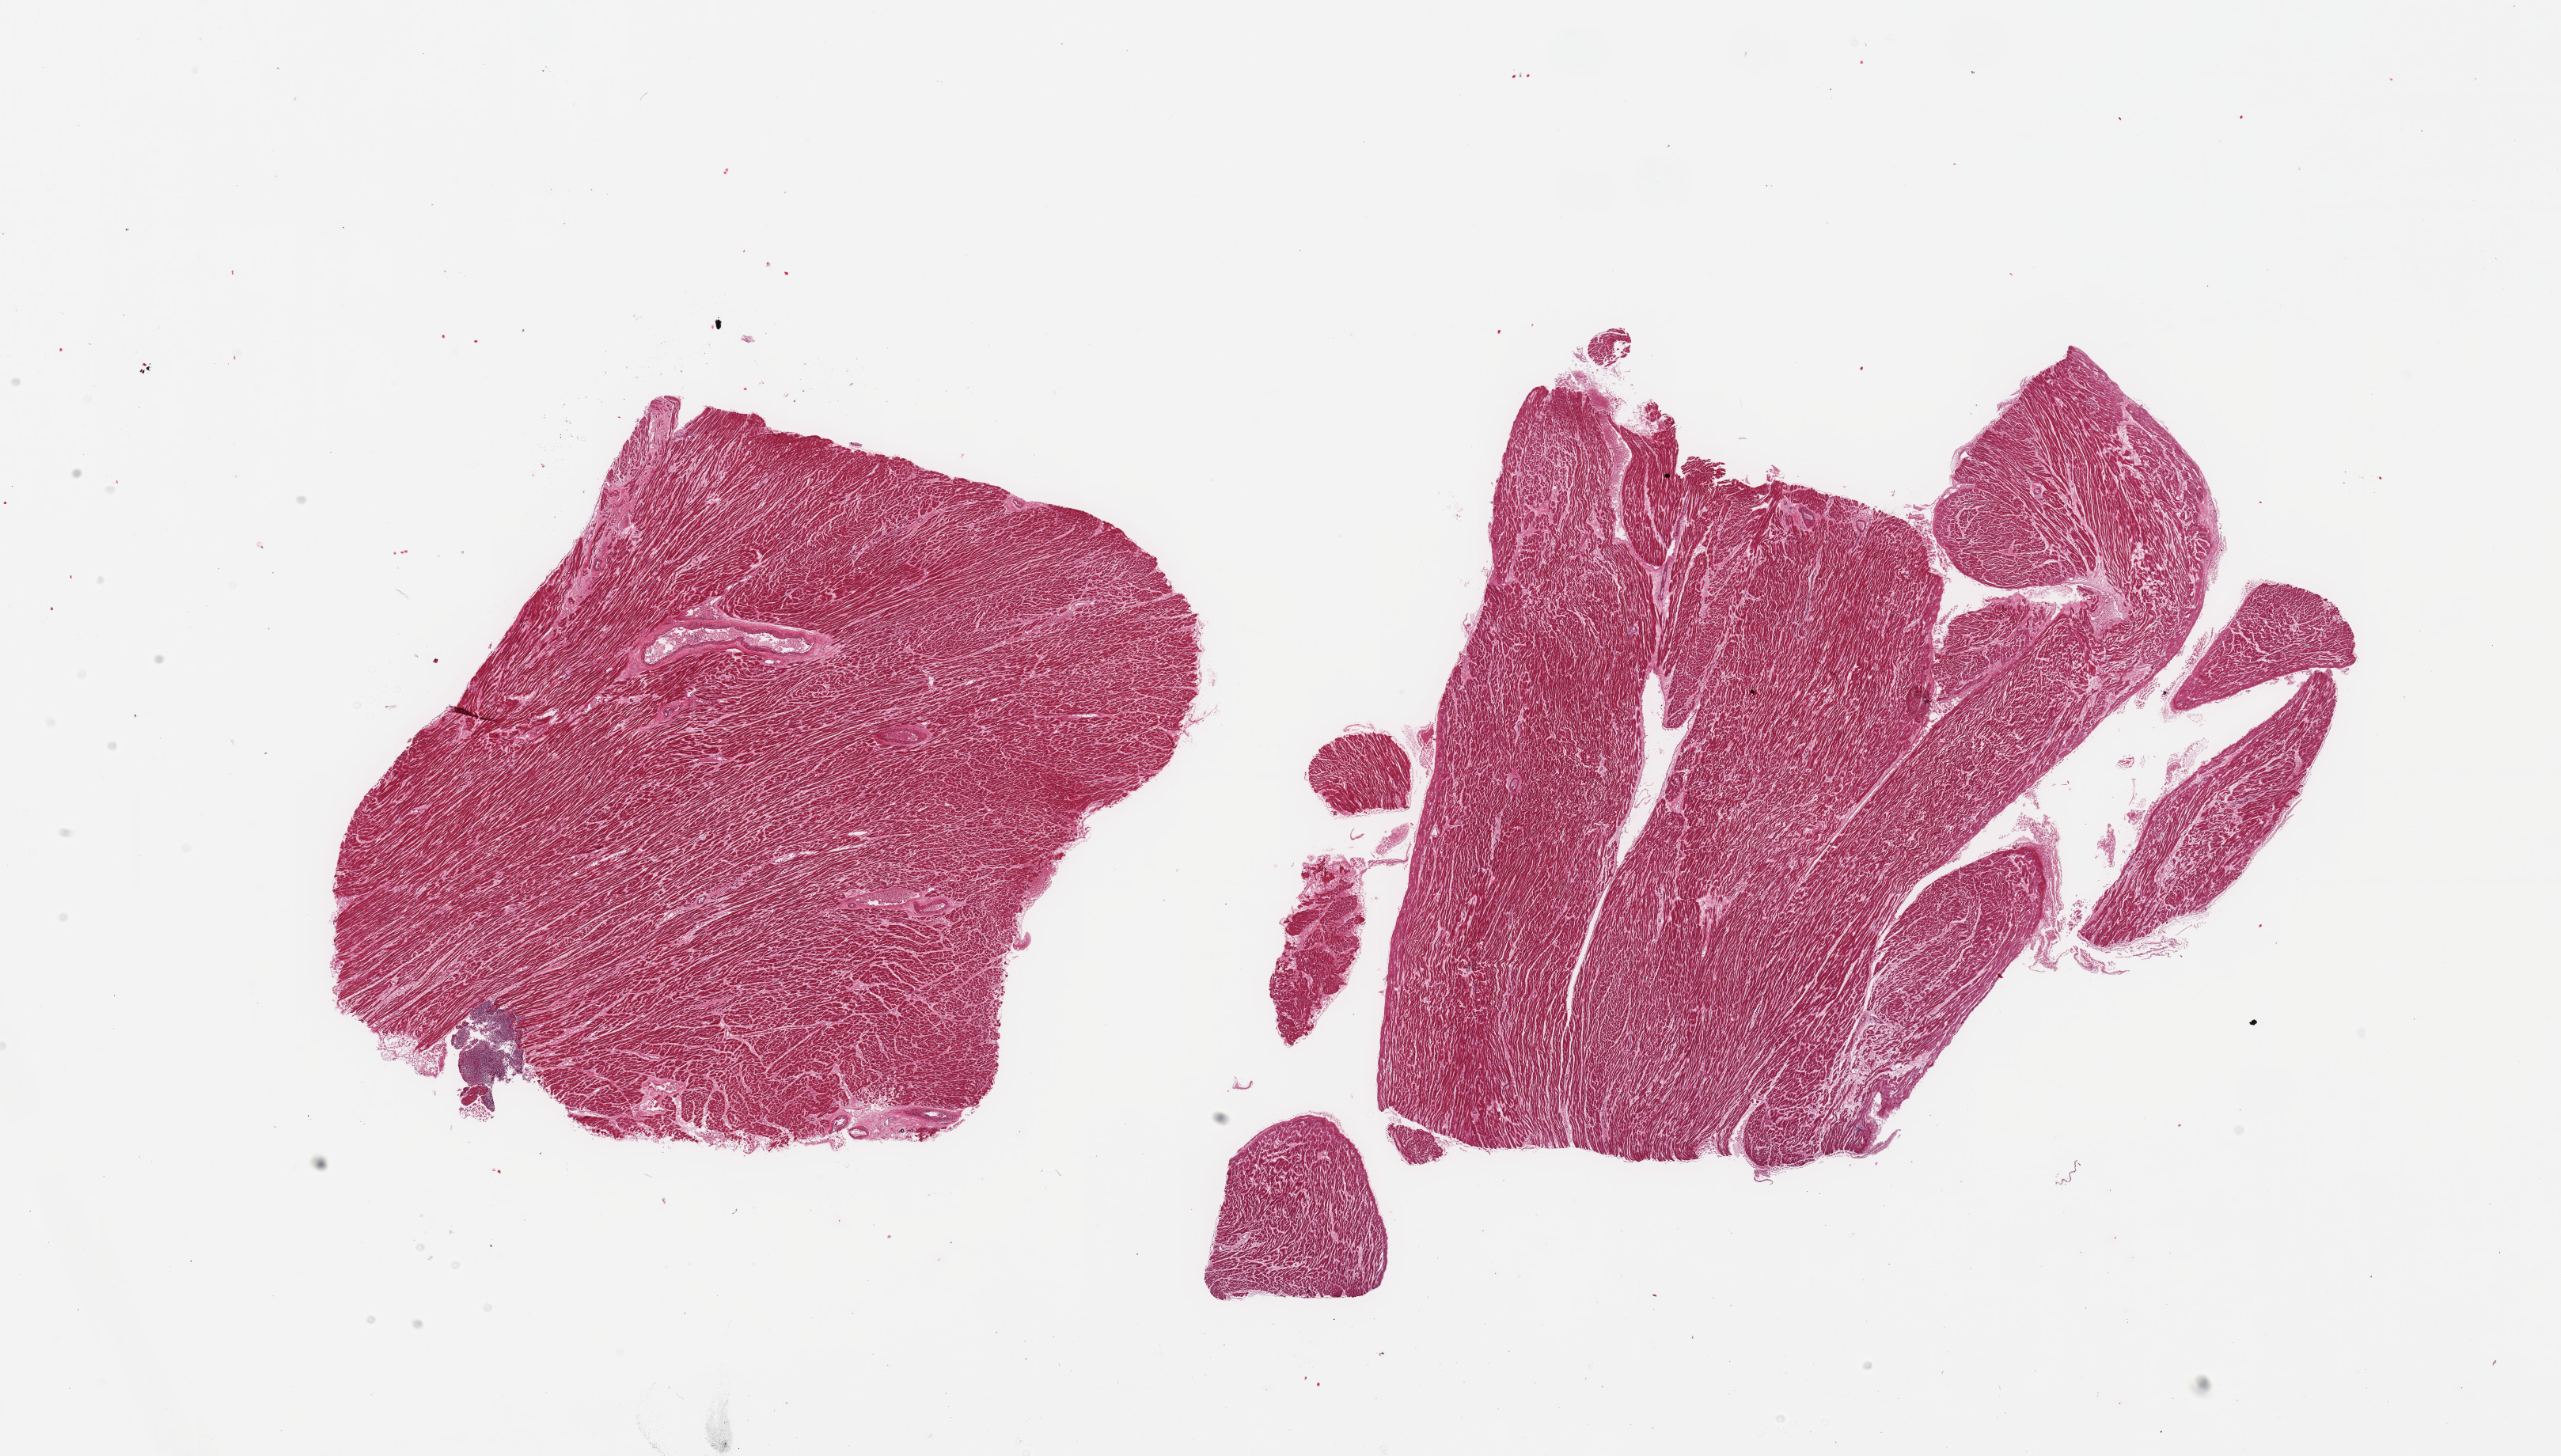
Digitized hematoxylin and eosin (H&E)-stained section — shown as a low-resolution overview of the whole scanned area (about 25.6 x 14.6 mm, from a 20x scan). PAXgene-fixed paraffin-embedded (PFPE) section. Section of heart (target tissue). Donor tissue sample. Donor sex: male.
Reviewer comment on this tissue sample: 2 pieces (some fragmentation); interstitial fibrosis with focal scarring.